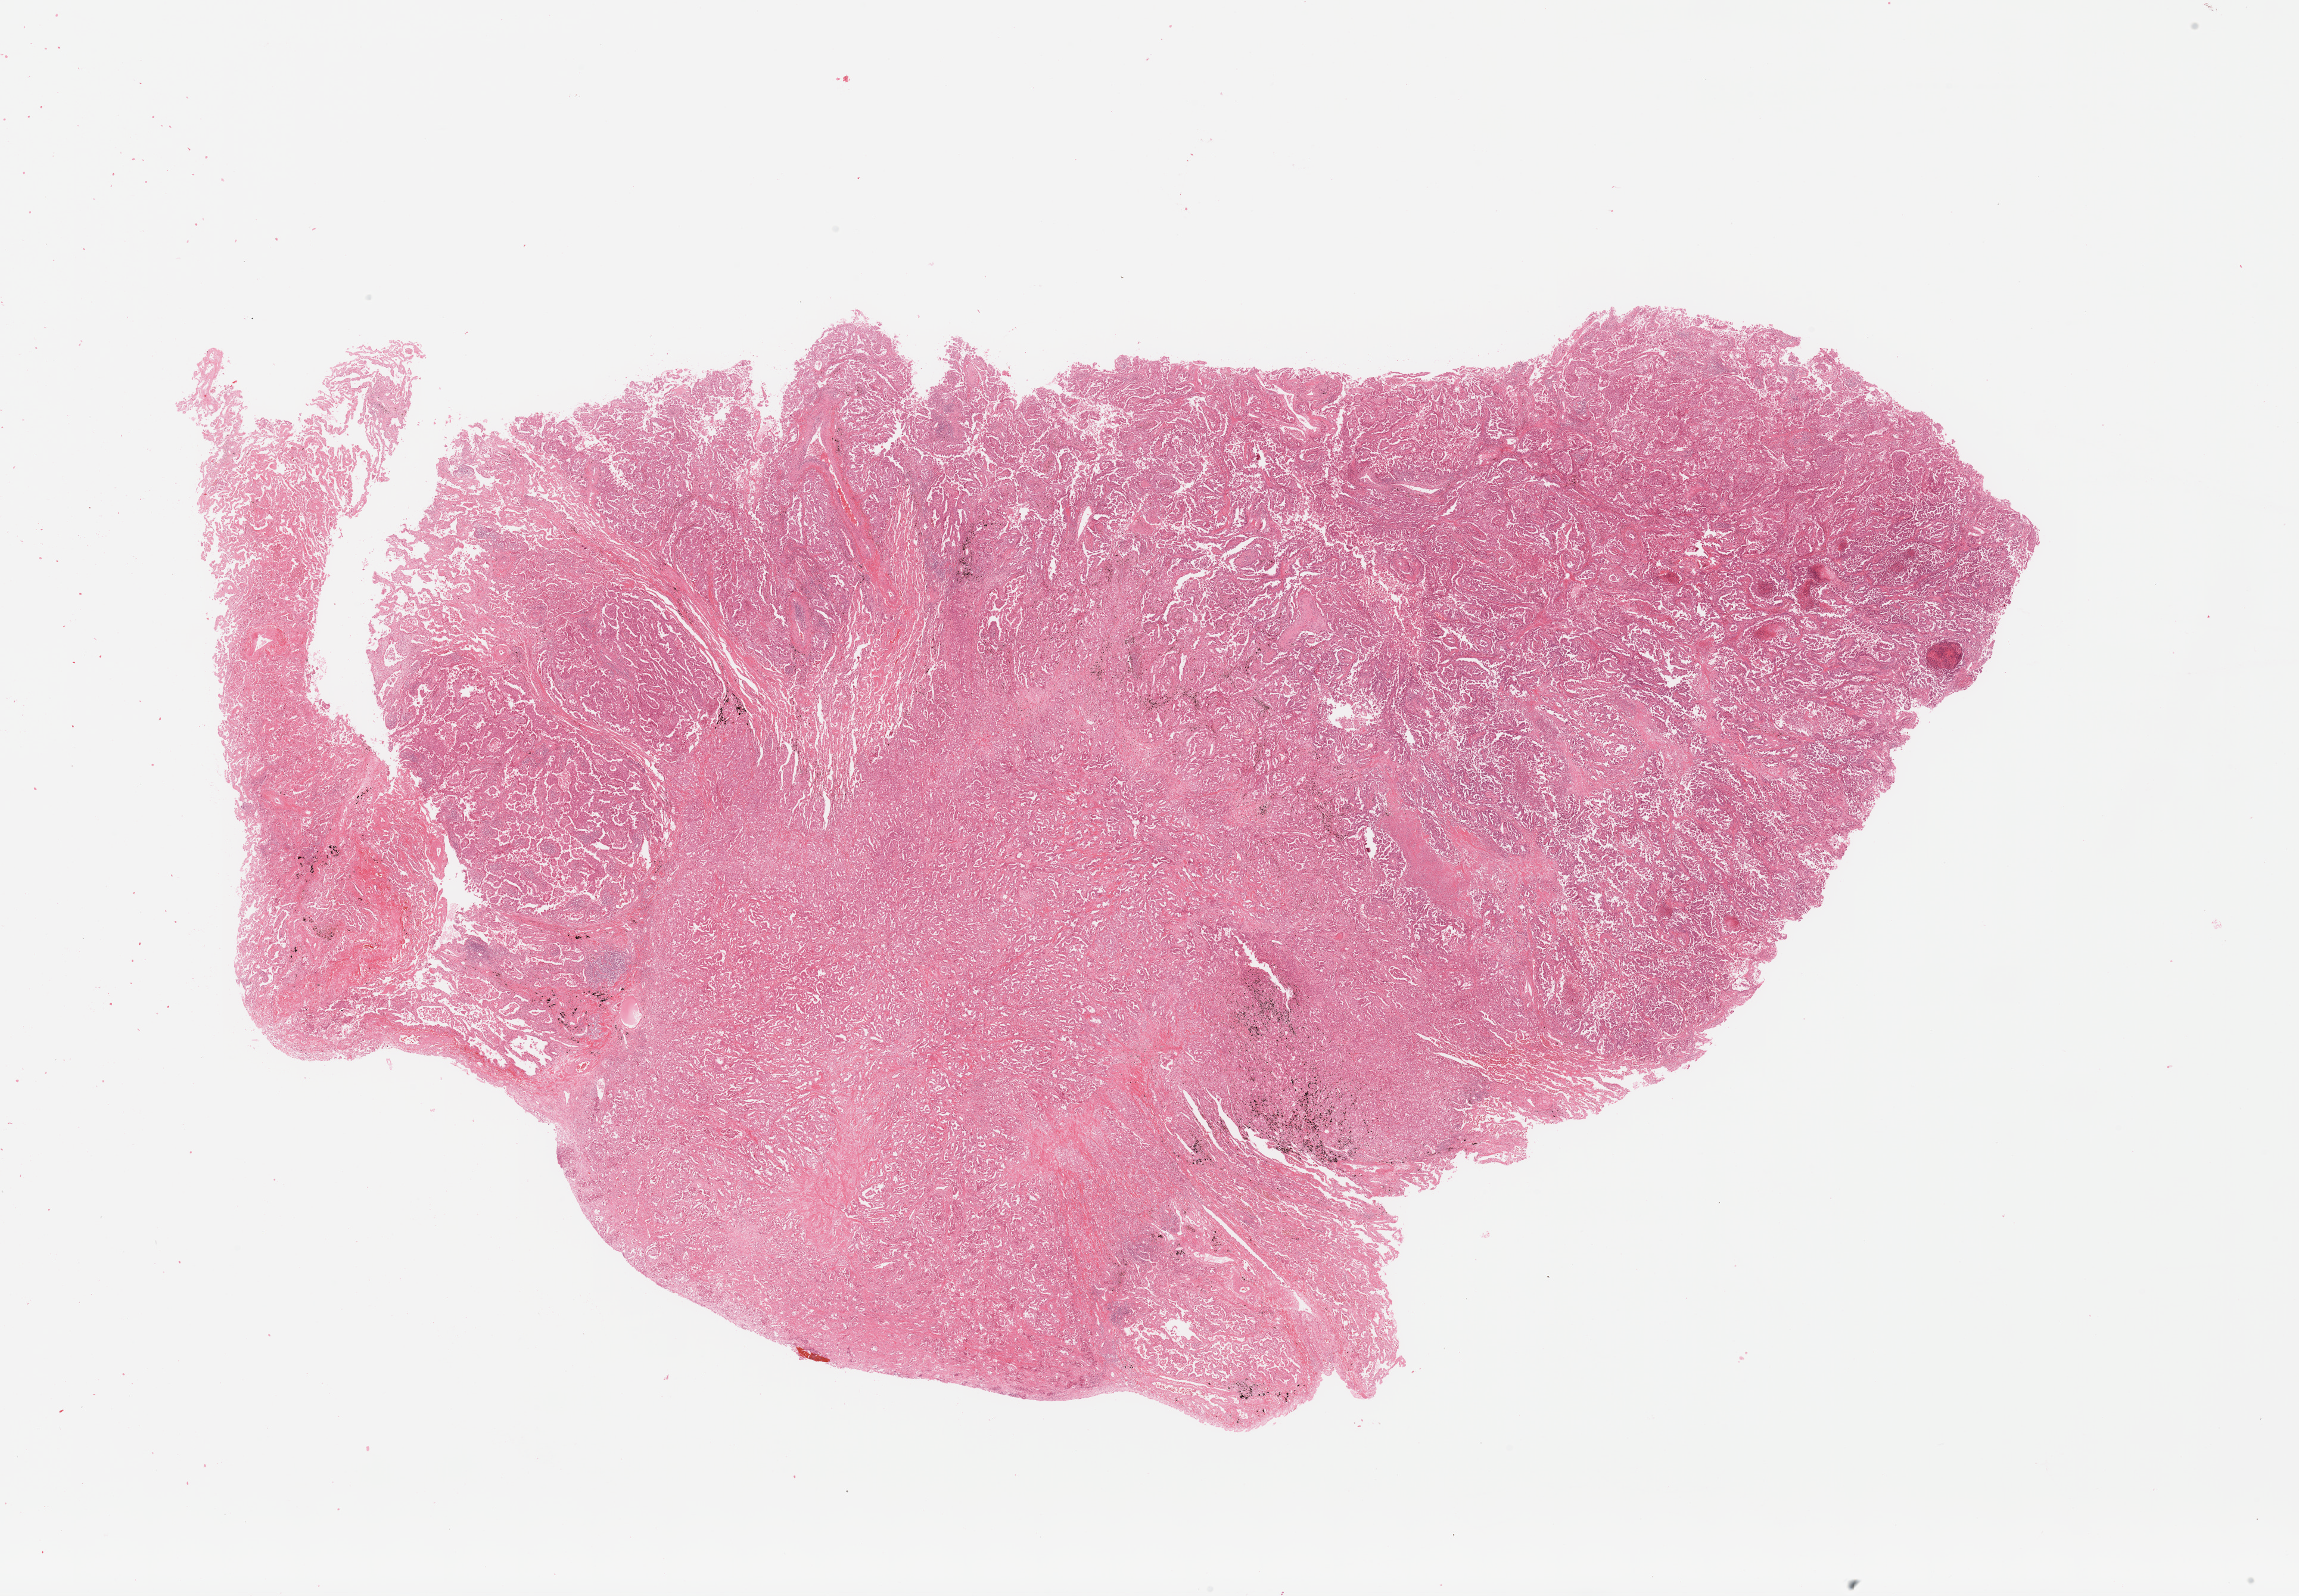
Digitized Hematoxylin and eosin (H&E) stained tissue section (whole slide) — low-resolution overview of the scanned area, about 30.5 x 21.2 mm (from a 20x scan). Tumour tissue sample, sampled site: lung. Male, 59 y/o. Histologic grade: G2 (moderately differentiated). Pathologist review of this section (percent, as recorded): tumour nuclei 80%, necrosis 2%.
- AJCC pathologic stage: IIIA
- histologic diagnosis: Adenocarcinoma, NOS